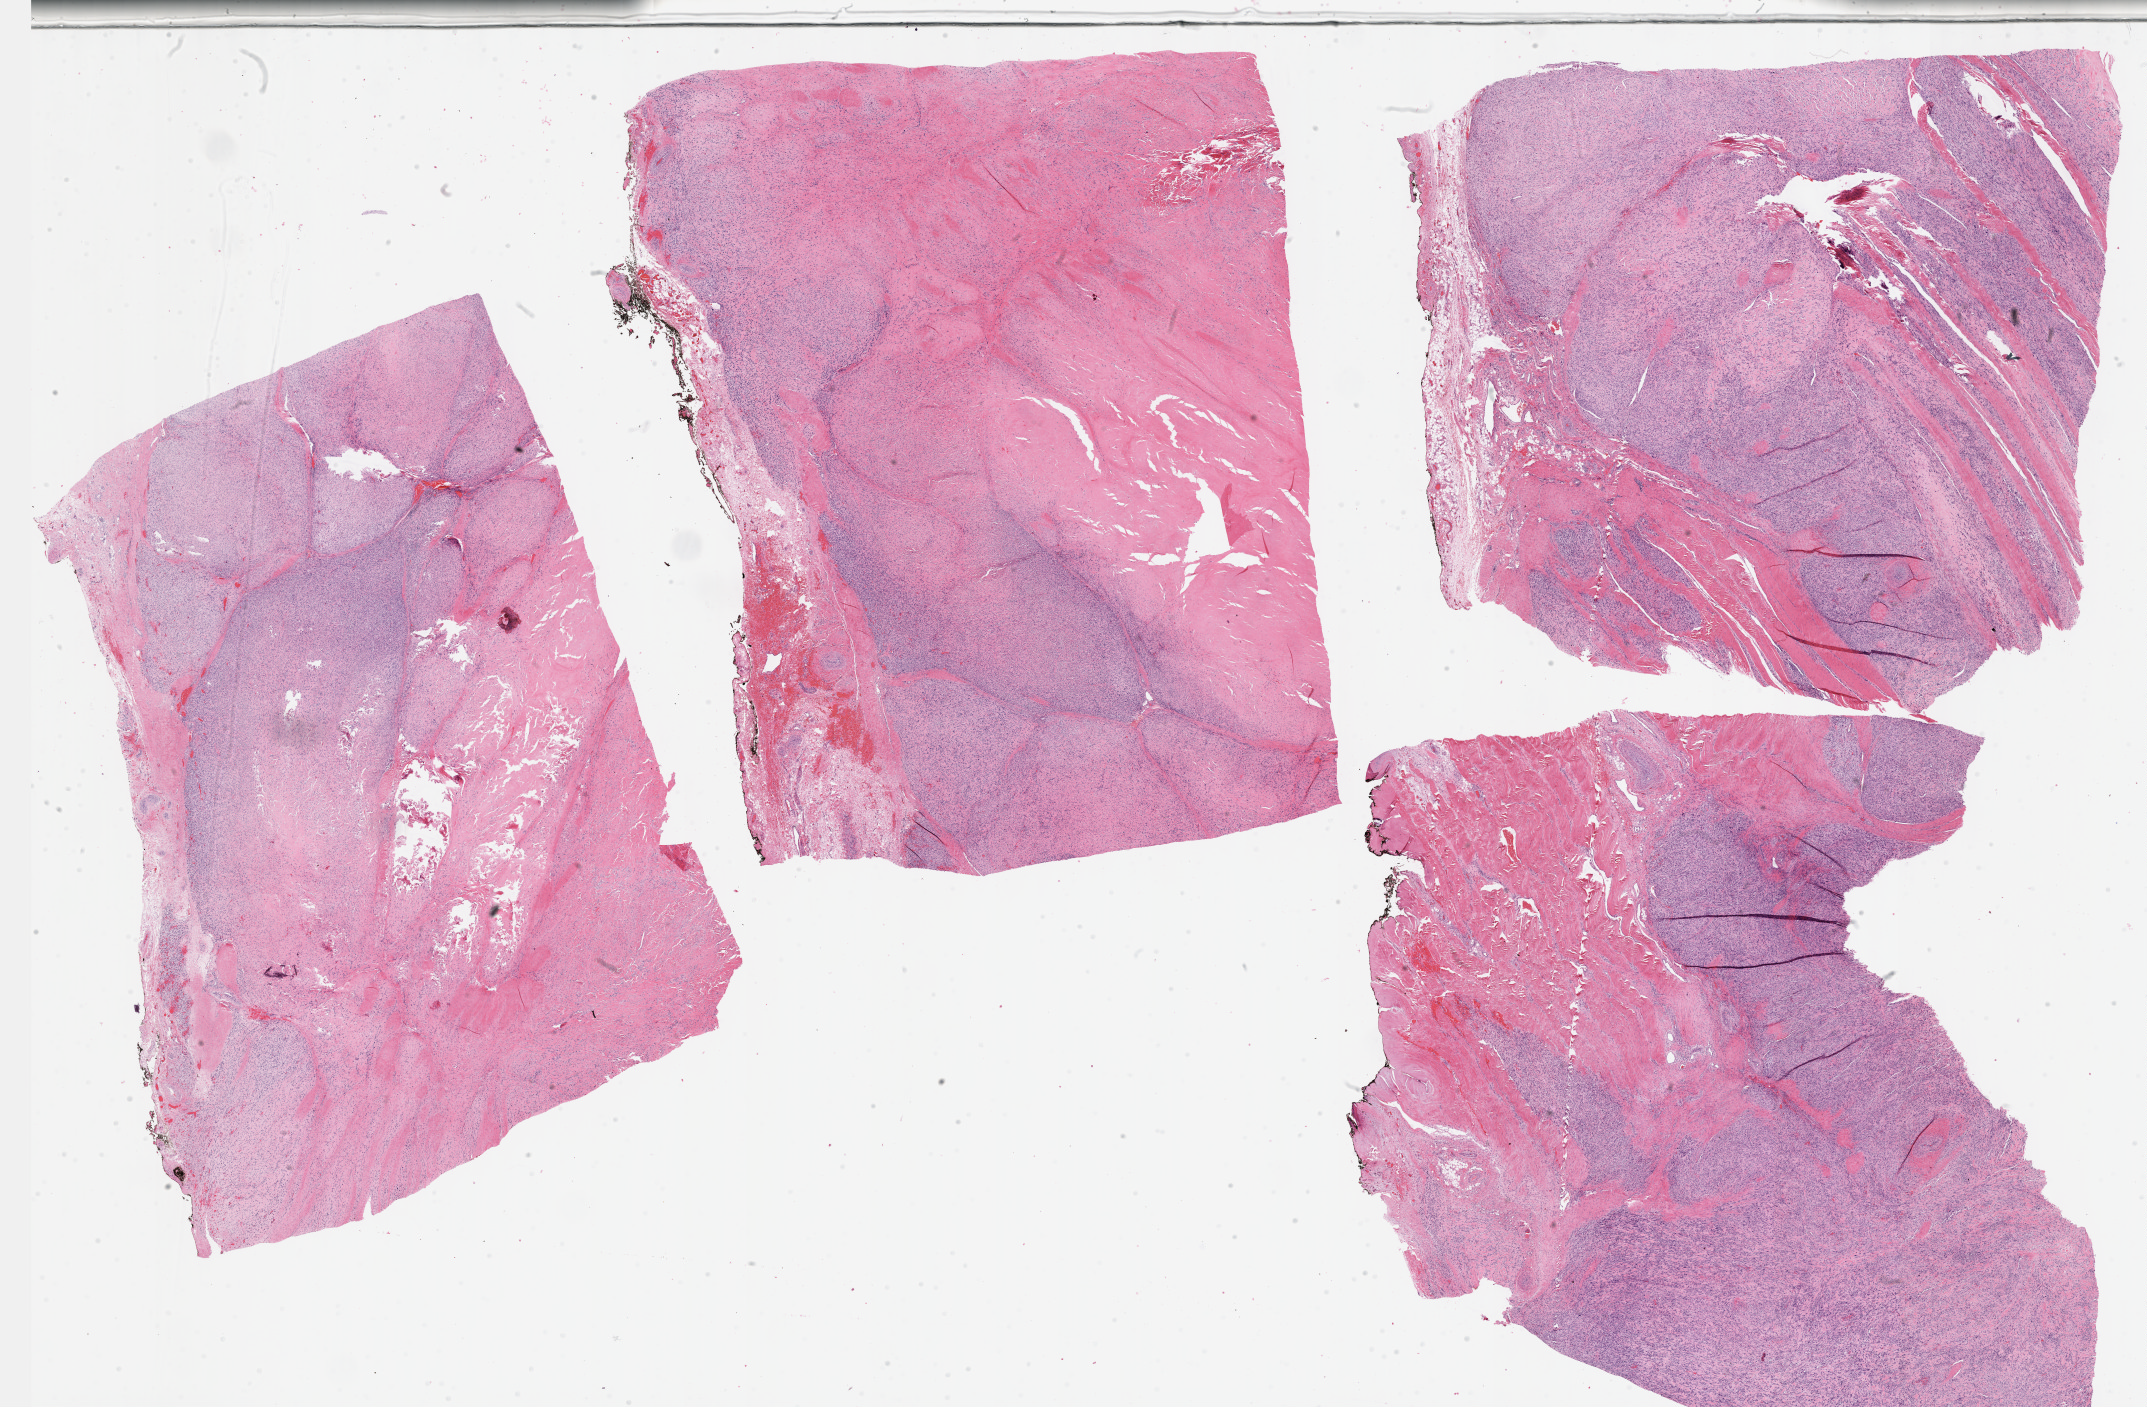
Digitized H&E tissue section (whole slide), a low-resolution overview of the entire scanned area, about 34.7 x 22.7 mm (acquisition: 40x scan), formalin-fixed paraffin-embedded (FFPE) diagnostic section, sample: primary tumour, connective, subcutaneous and other soft tissues. Male patient; age at initial diagnosis 74 years.
- diagnosis: Leiomyosarcoma, NOS (connective, subcutaneous and other soft tissues of lower limb and hip)